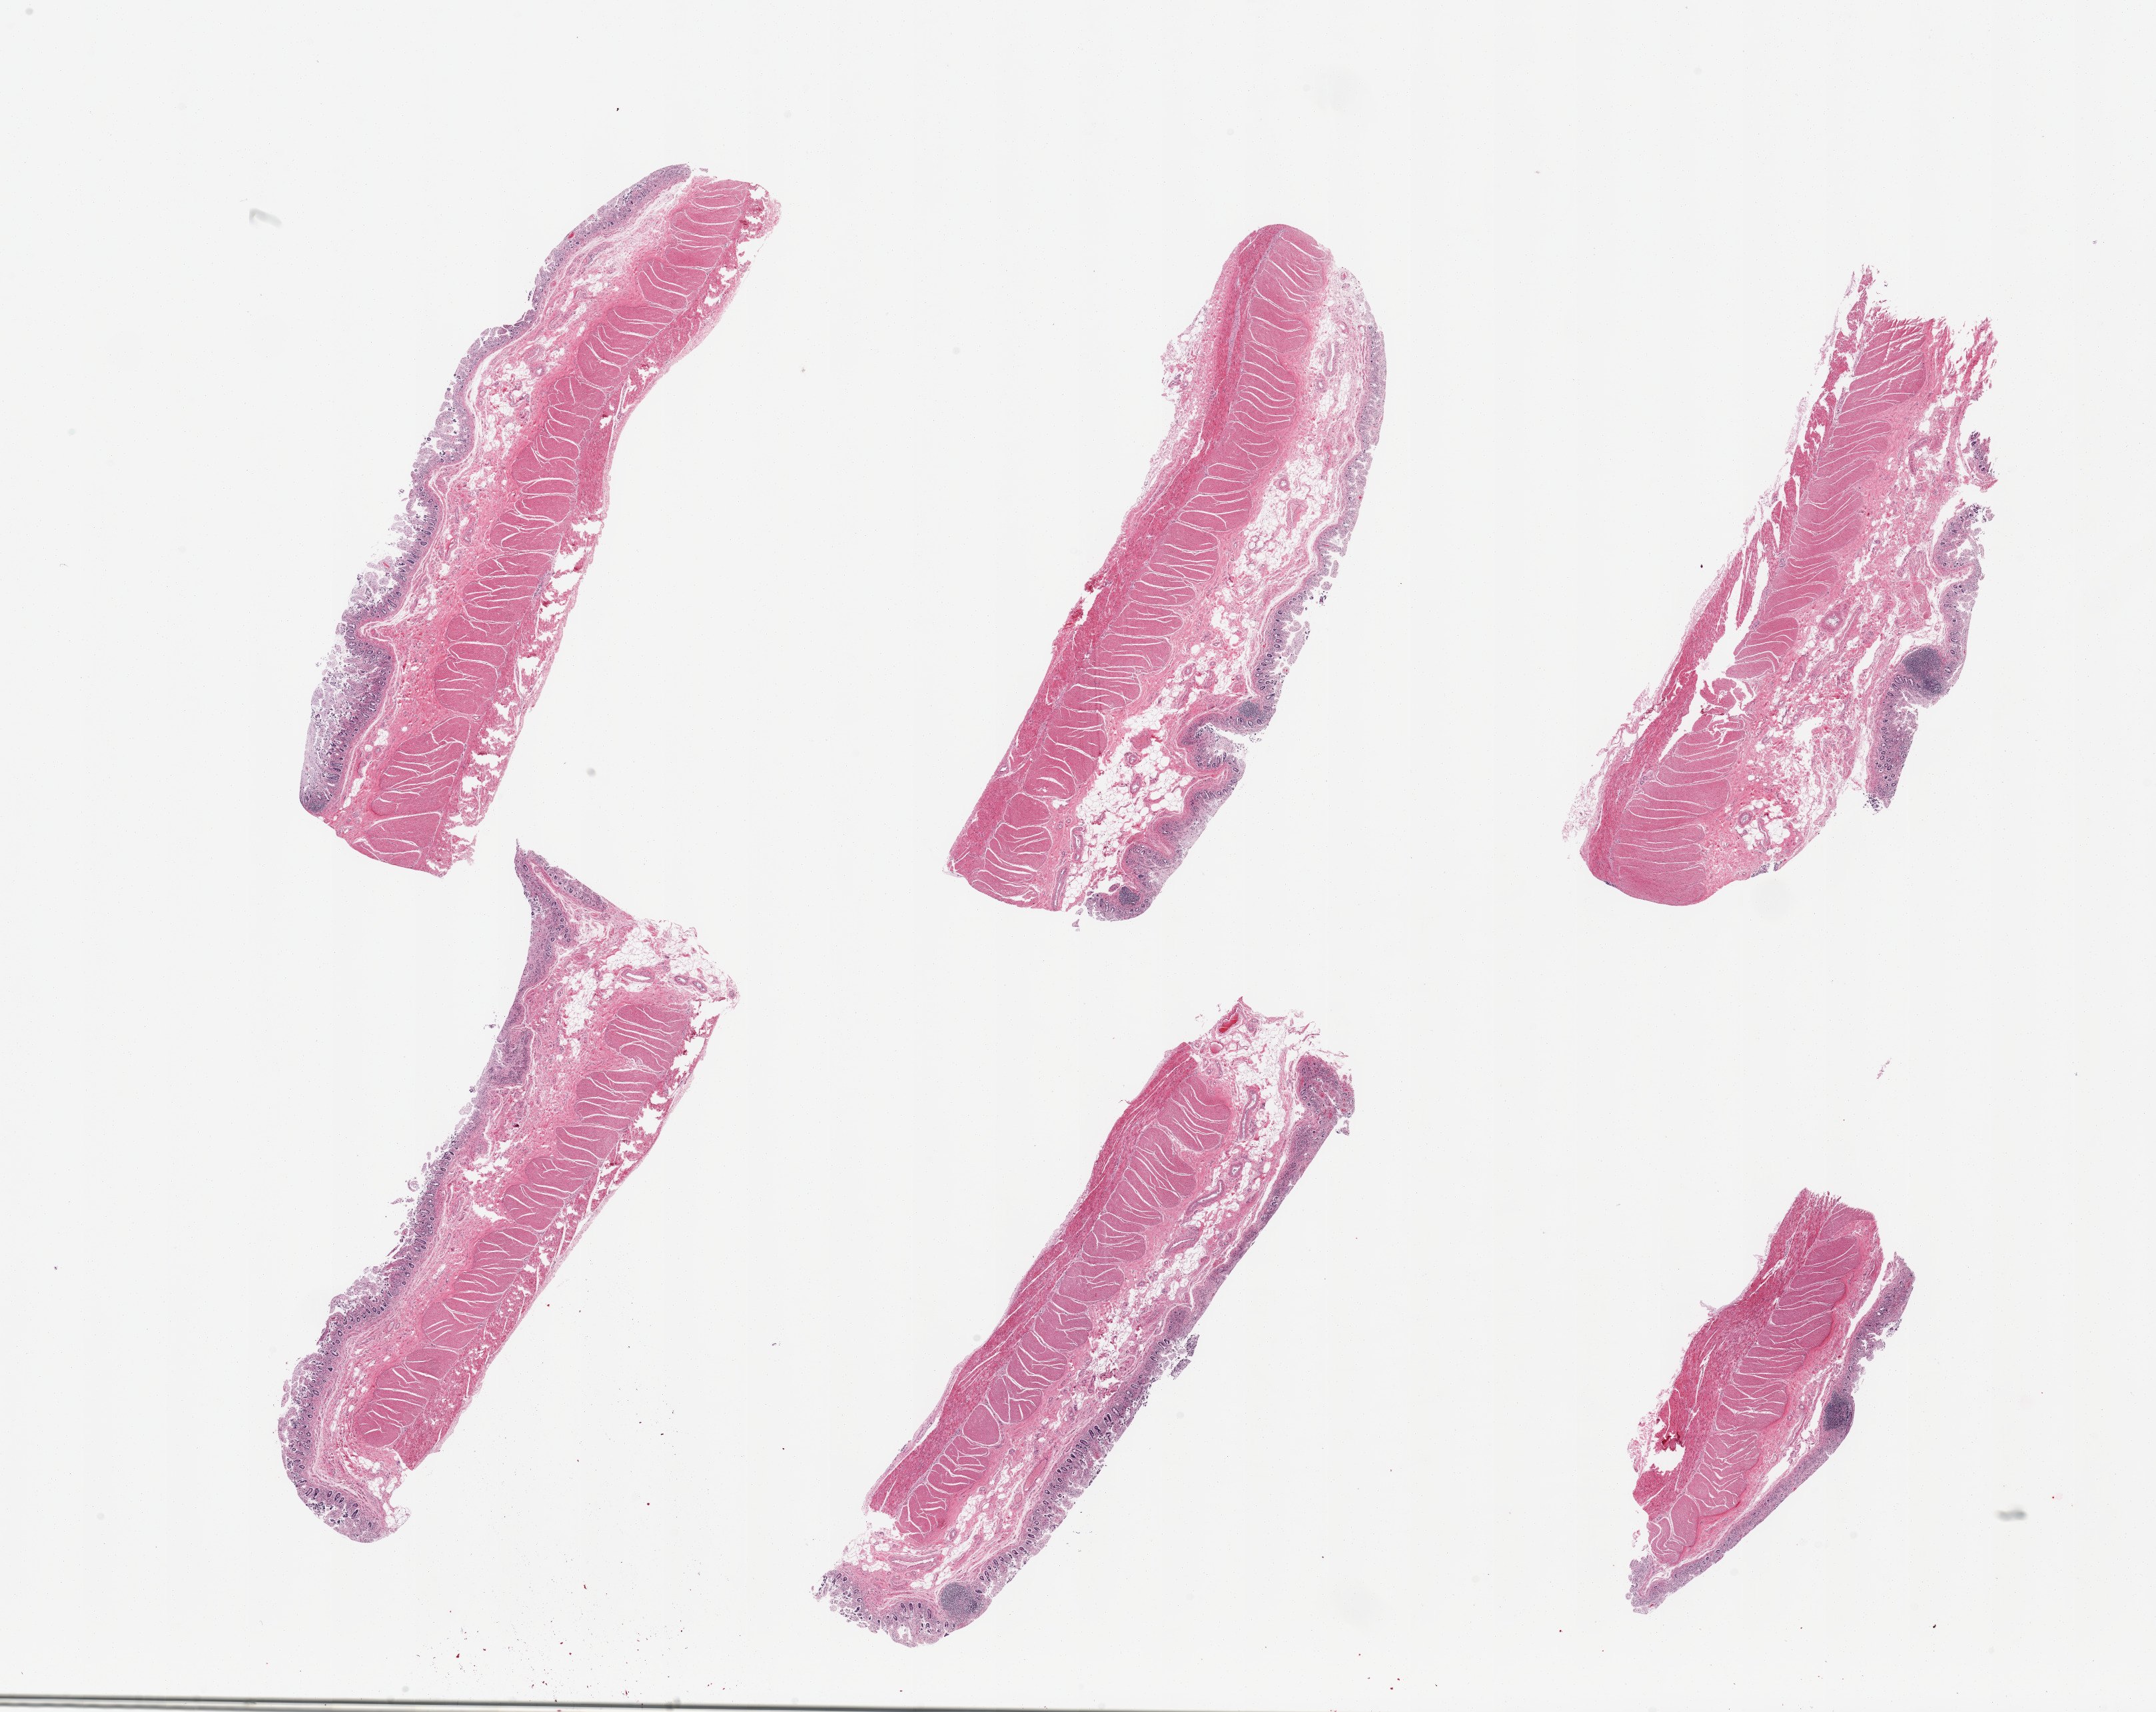
Digitized hematoxylin and eosin (H&E)-stained section — low-resolution overview of the scanned area, about 25.6 x 20.3 mm, PAXgene-fixed paraffin-embedded (PFPE) section, target tissue: ileum, tissue donor sample. Donor: male.
Pathologist's review note for this sample: 6 pieces; only 2 small lymphoid nodules in mucosa; full thickness of wall sampled.